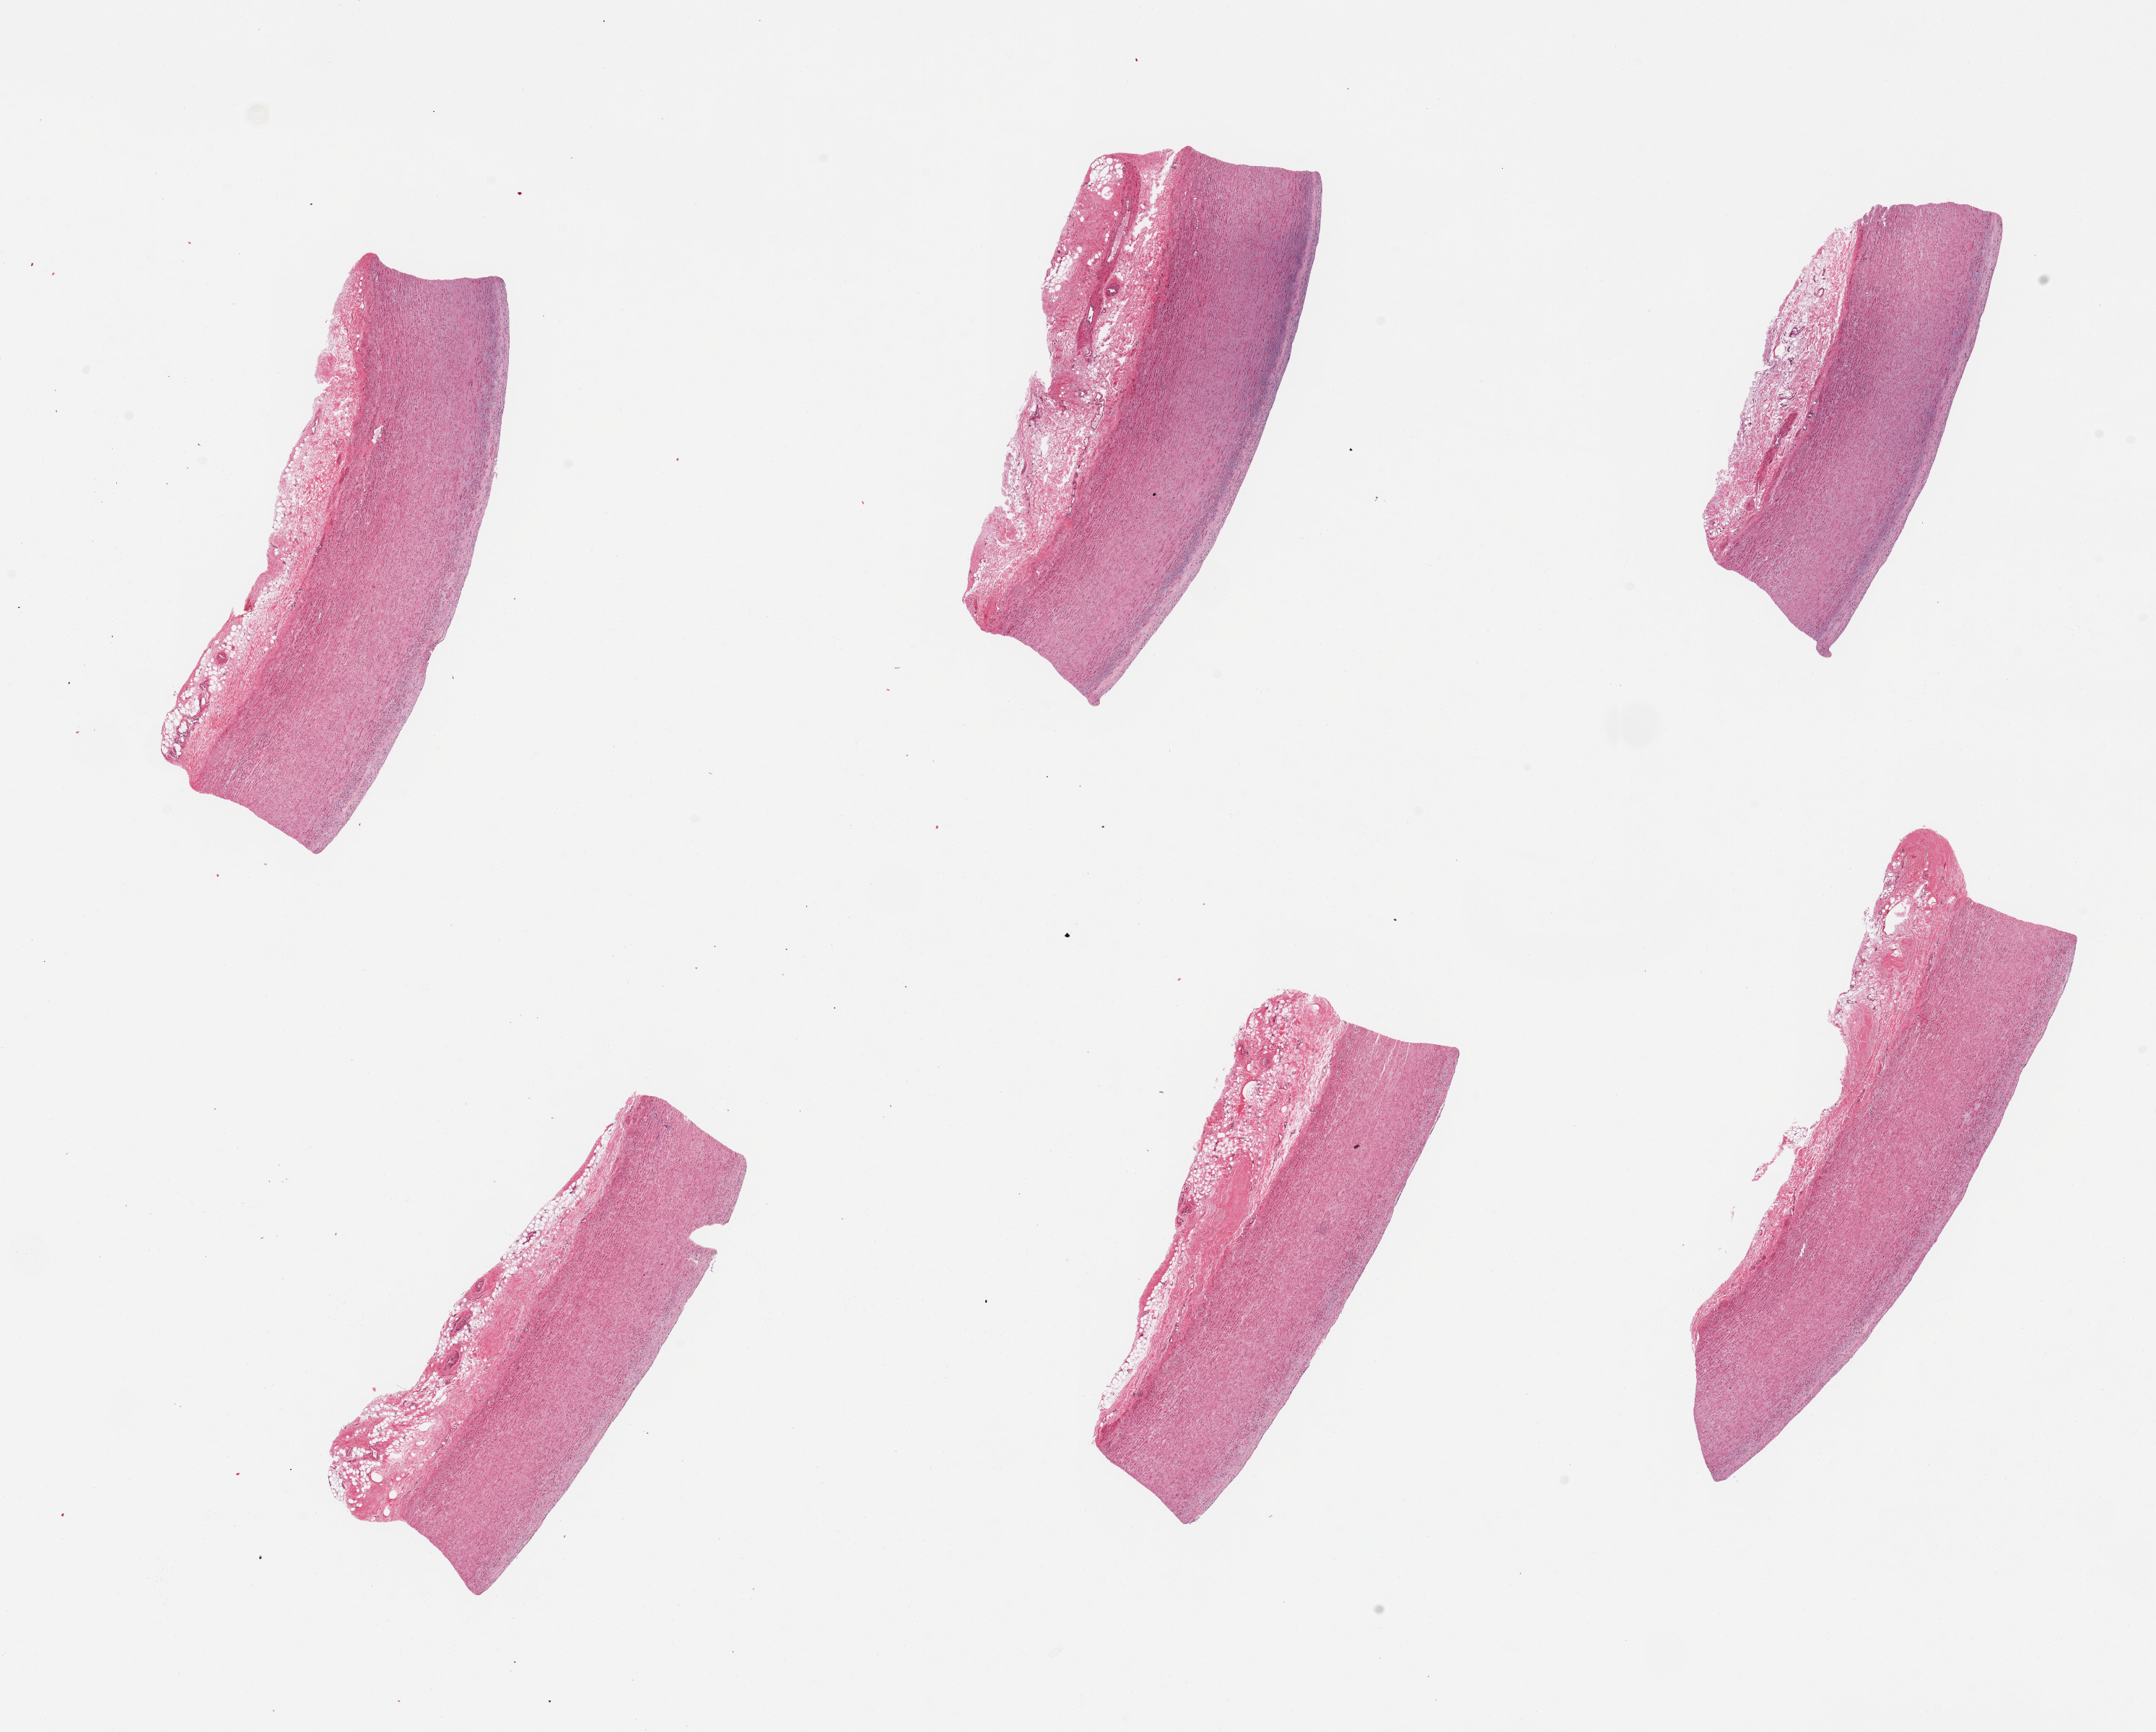
Digitized haematoxylin and eosin-stained section, a low-resolution overview of the entire scanned area, about 23.6 x 19.0 mm (from a 20x scan); PAXgene-fixed paraffin-embedded (PFPE) section; target tissue: aorta; tissue donor sample. Donor sex: male.
- pathologist's review note for this sample: 6 pieces; minimal plaque; up to 1 mm thick fibrofatty adventitia on all